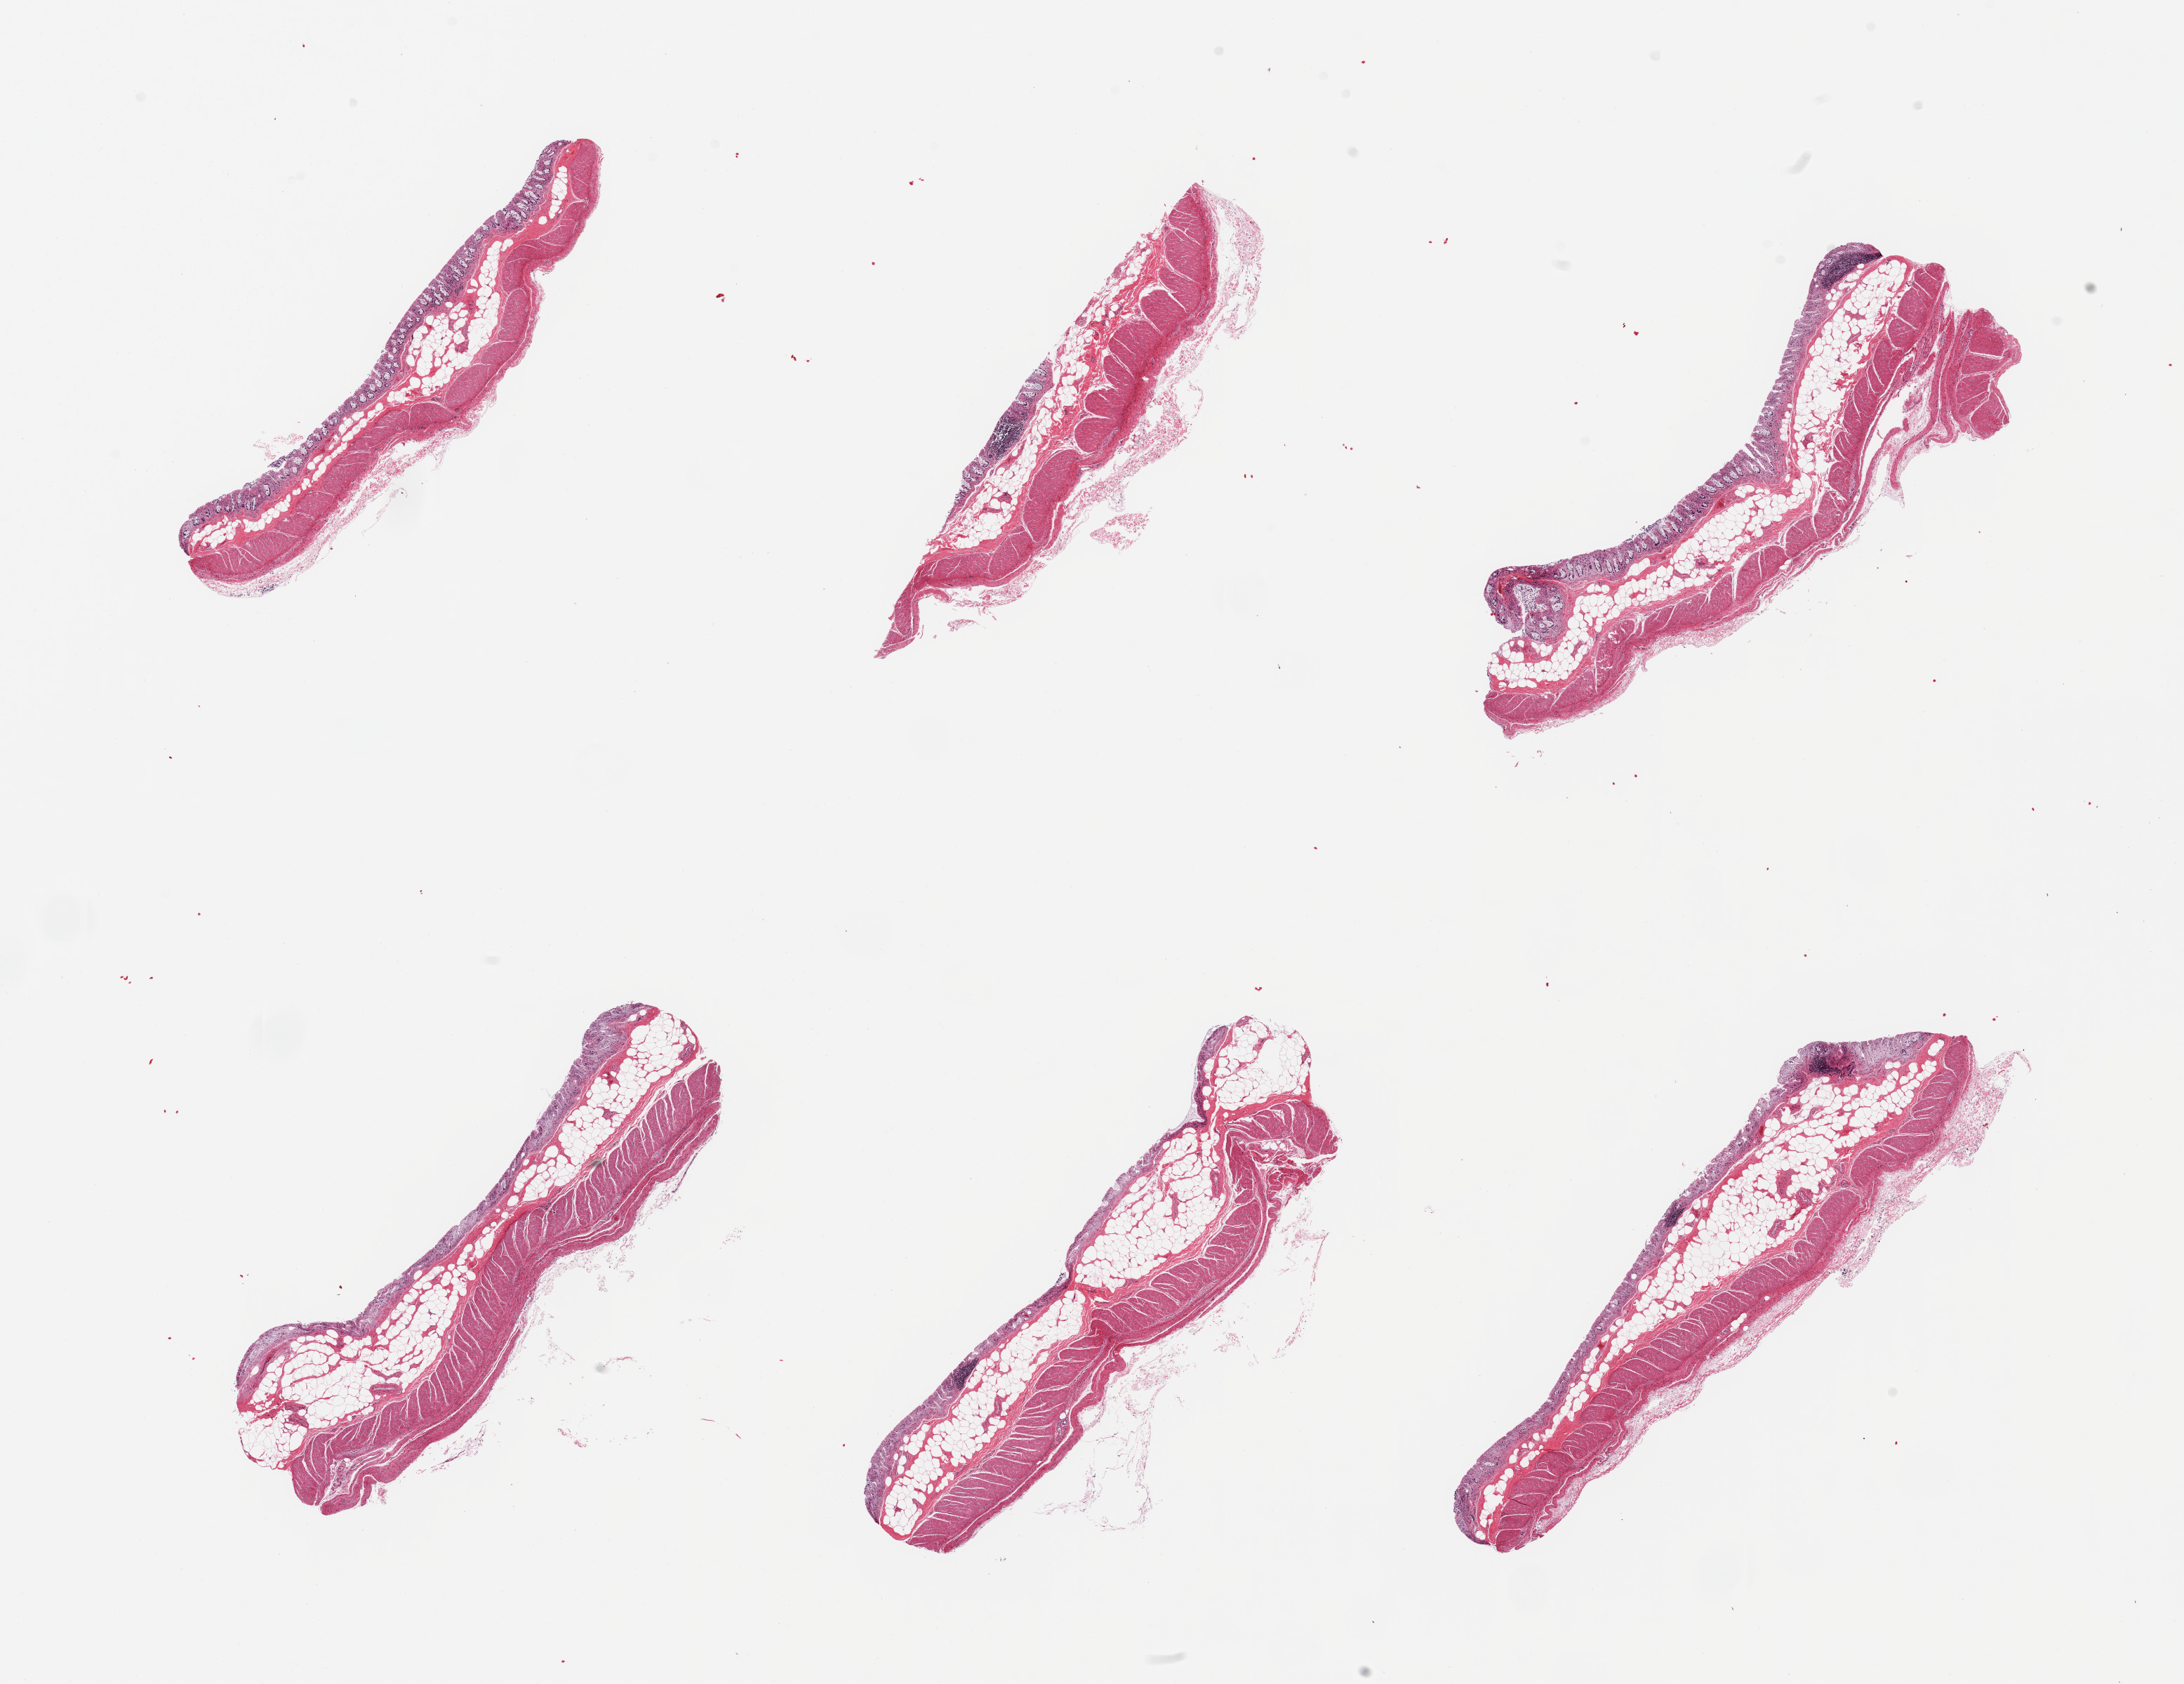
Haematoxylin and eosin whole-slide image, brightfield — shown as a low-resolution overview of the whole scanned area (about 24.6 x 19.0 mm), PAXgene-fixed, paraffin-embedded tissue, target tissue: transverse colon, donor tissue sample.
Review note (as recorded): 6 pieces; severely autolyzed mucosa, muscularis is better preserved.